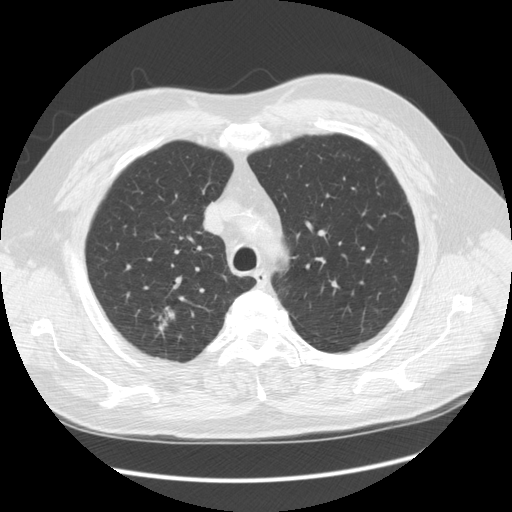
Low-dose screening chest CT, one axial slice. Position 84 of 108 along the scan axis. 120 kVp. Lung window (W 1500 / L -600 HU). 2.5 mm slice thickness. 512 × 512 image matrix, field of view 380 × 380 mm.
Structures marked on this image (expert manual segmentation):
- lesion 1 (tumor, upper lobe of right lung): bounding box (x1, y1, x2, y2) in pixels: (158, 306, 175, 335)